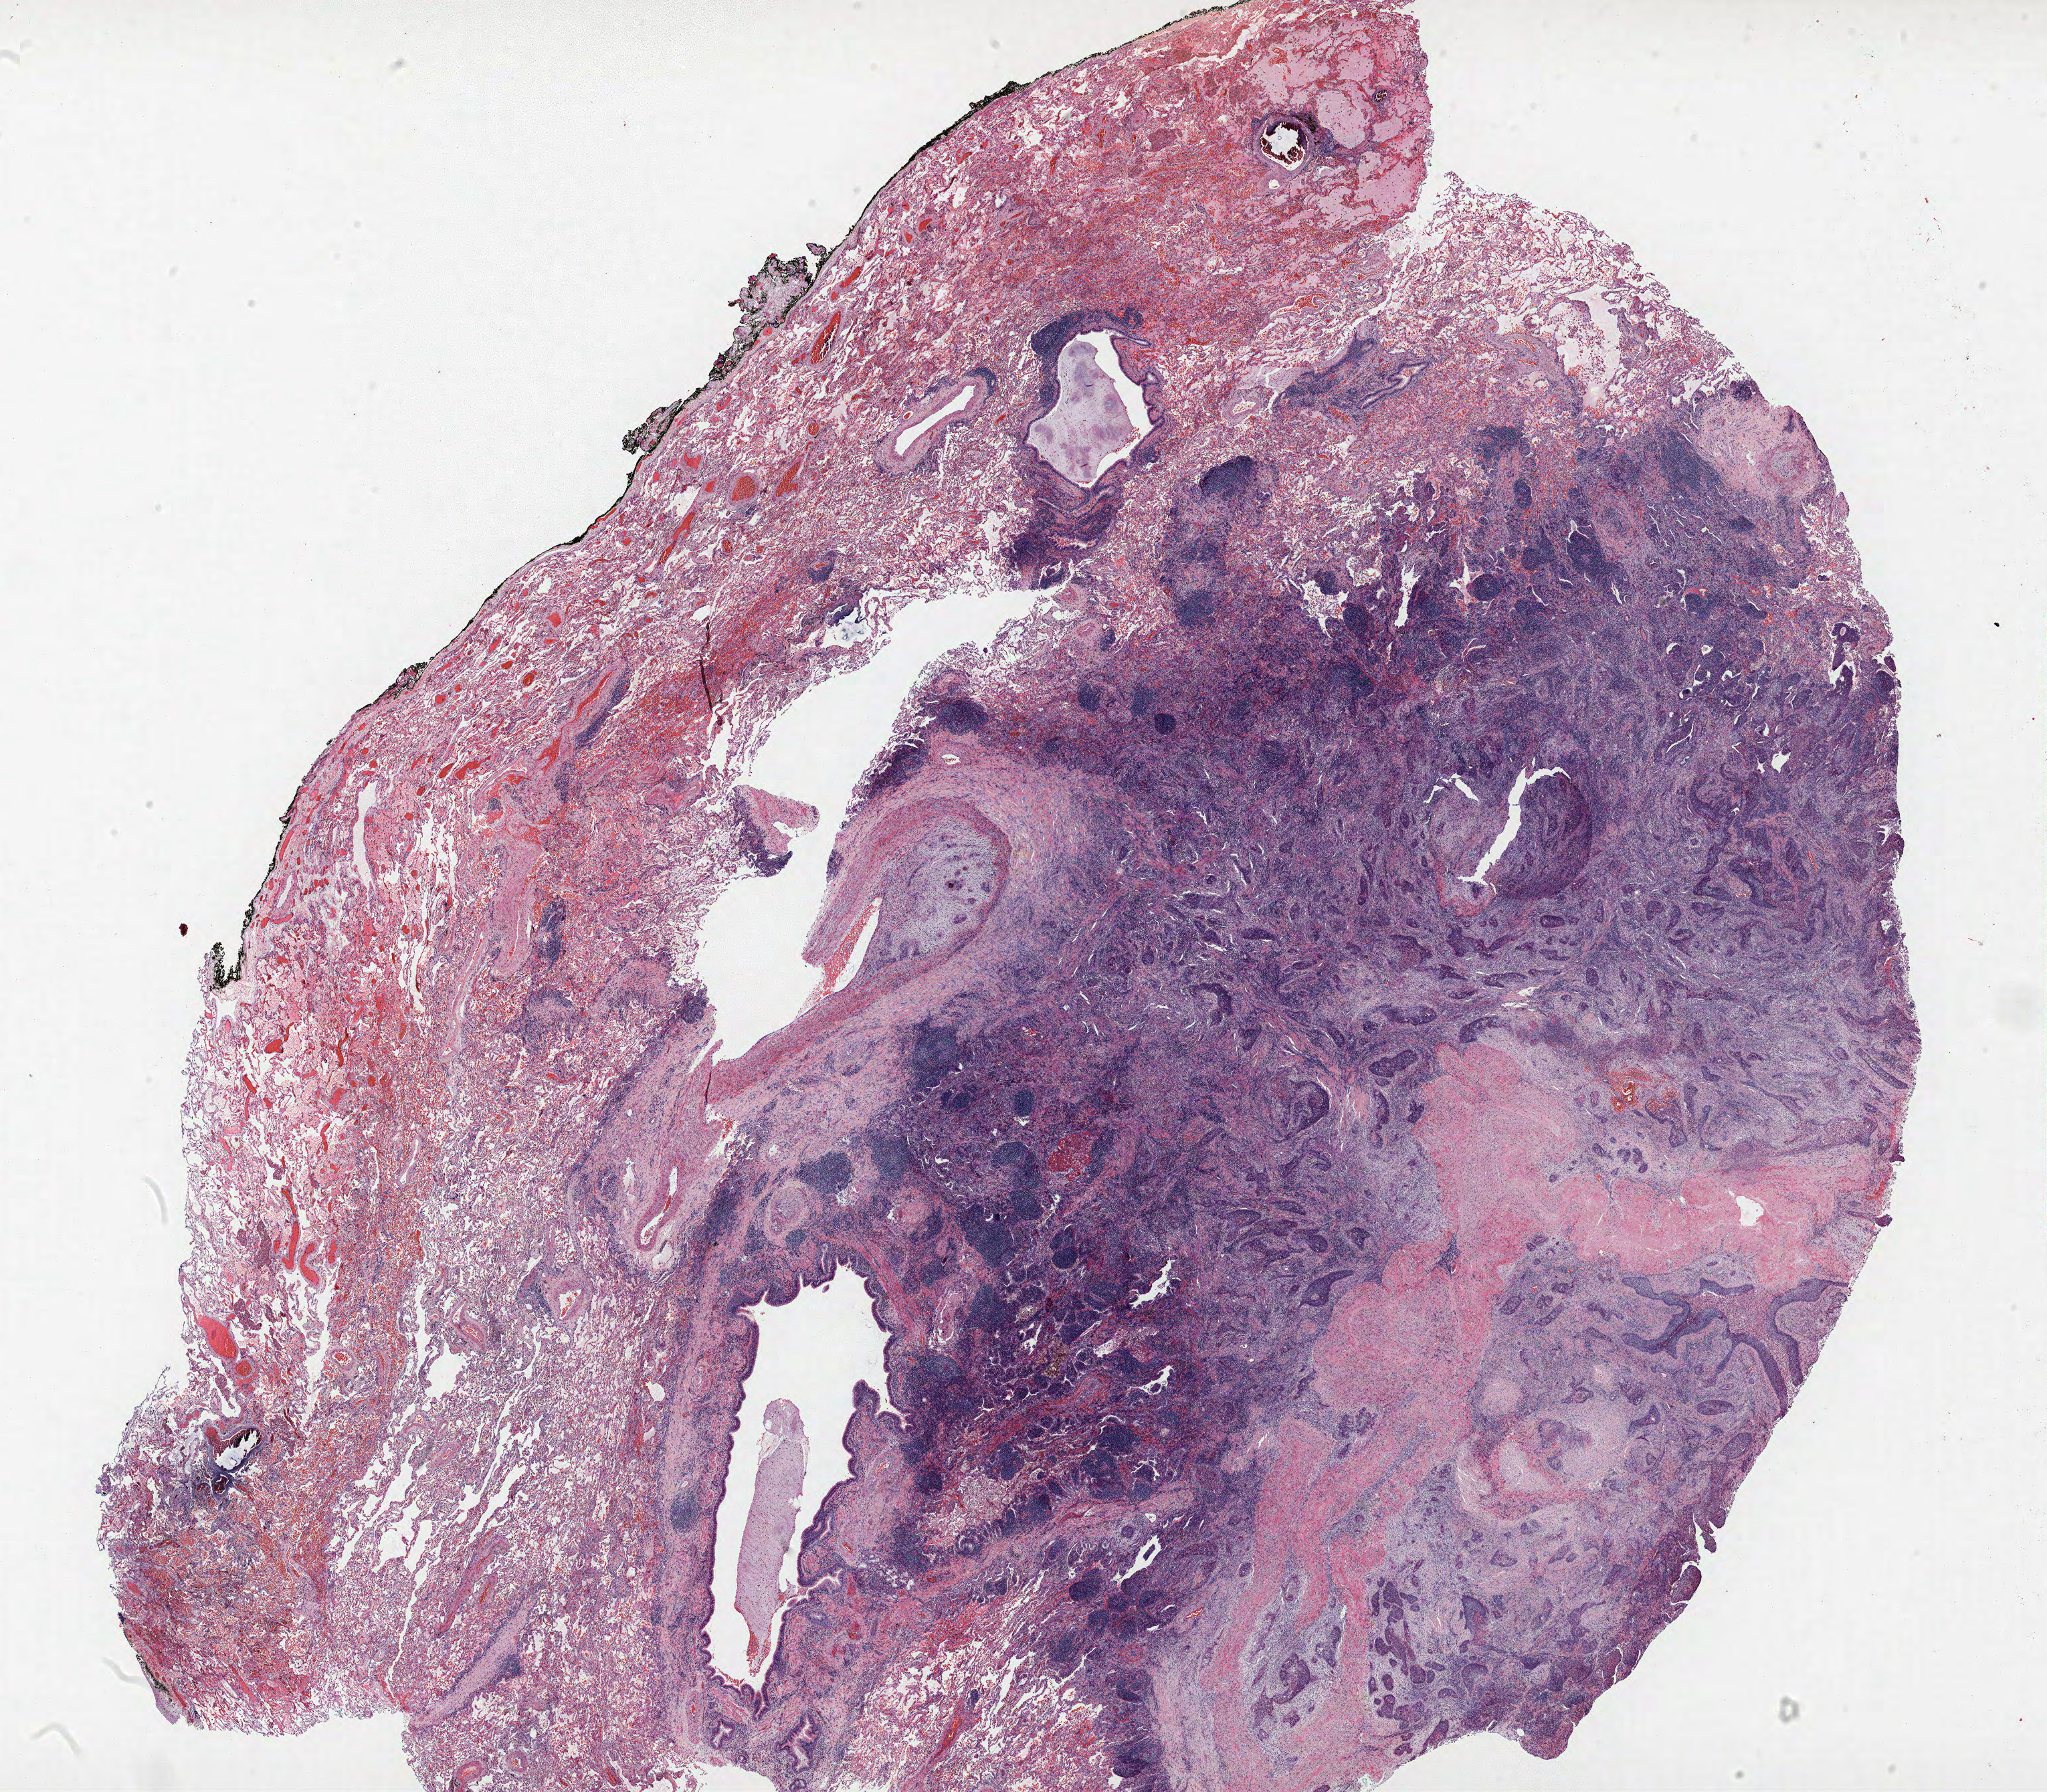
Hematoxylin and eosin (H&E) stained whole-slide image, shown as a low-resolution overview of the whole scanned area (about 24.5 x 21.4 mm); FFPE section; lung. Male patient, aged 68 at enrolment. Current smoker at enrolment. Grade: poorly differentiated (G3).
- participant's lung-cancer diagnosis: Squamous cell carcinoma, NOS
- stage (AJCC 6th edition): IA
- tumour size (pathology): 20 mm
- primary tumour location (clinical record): left upper lobe